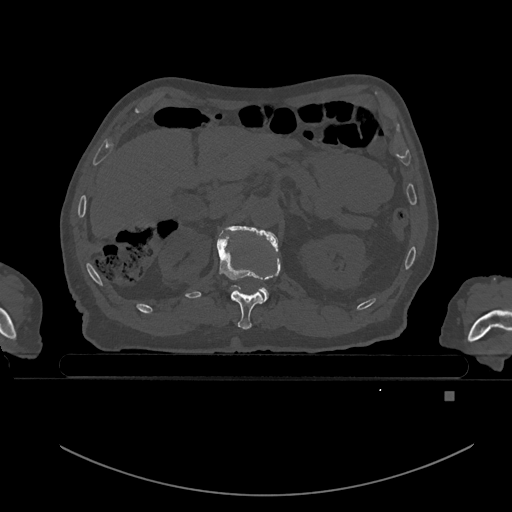
CT including the spine, one axial slice. Slice 1 of 969 in the series (ordered by position). Bone window (W 1800 / L 400 HU). 0.5 mm slice thickness. 512 × 512 image matrix, field of view 456 × 456 mm. Patient: male, 82 years. Case-level facts recorded for this patient, not image findings: primary cancer: prostate; vertebrae with lytic lesions (as recorded): T11, T9, T8, T2.
Annotated regions visible in this slice (semi-automatic segmentation, software-assisted and operator-edited):
- T11 vertebra: bounding box <217,228,278,329> (left, top, right, bottom; pixels)